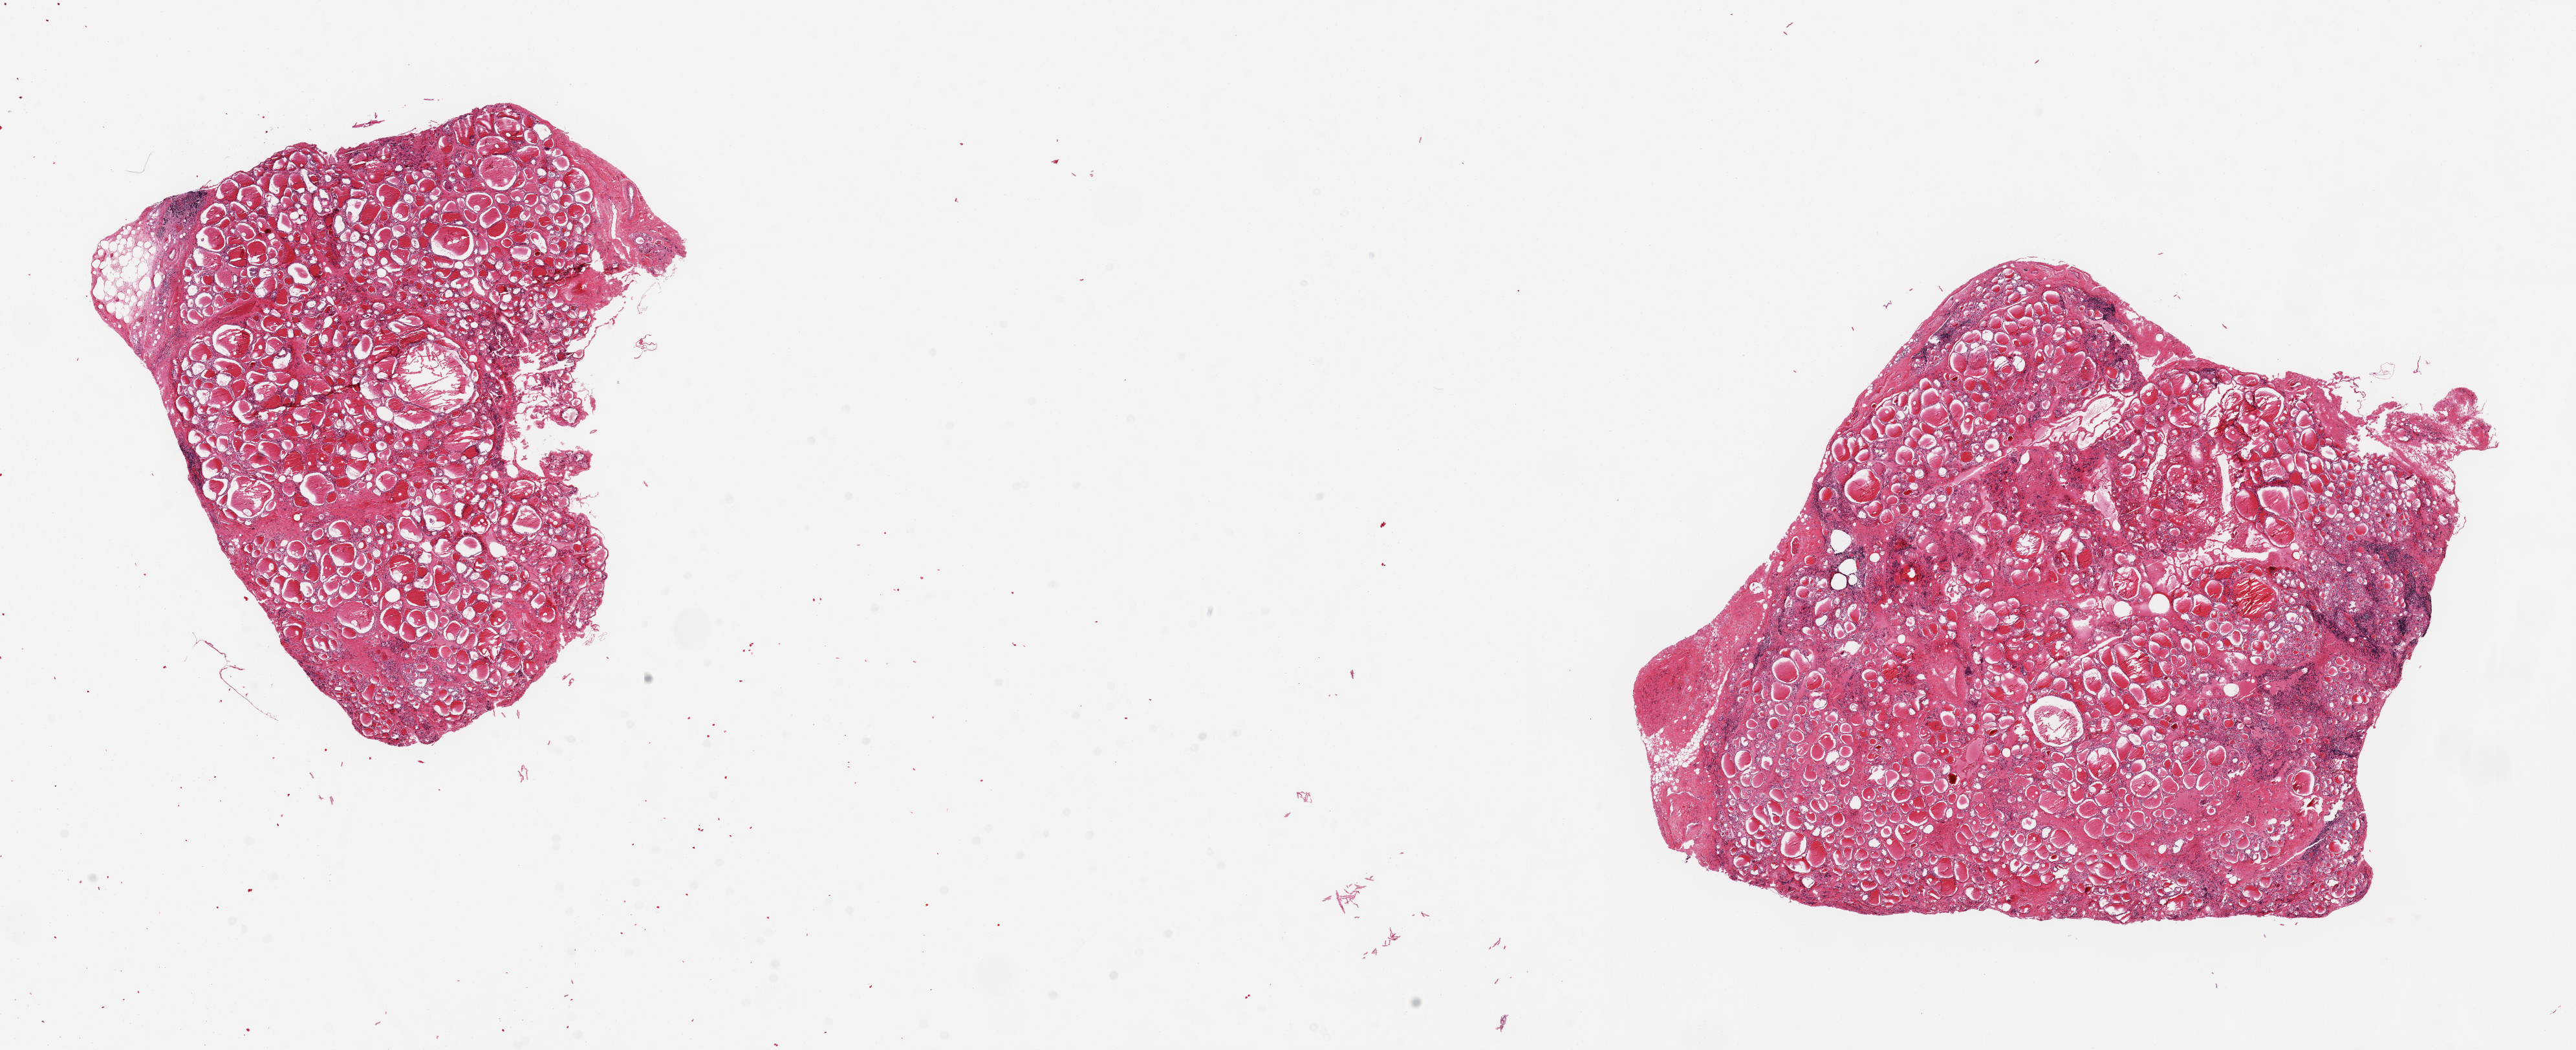
Digitized hematoxylin and eosin (H&E)-stained section, brightfield — low-resolution overview of the scanned area, about 31.5 x 12.8 mm, PAXgene-fixed, paraffin-embedded tissue, target tissue: thyroid, tissue donor sample. Female donor.
Pathologist's review note for this sample: 2 pieces, 8x7 & 10.5X8mm; focal lymphoid infiltrates.